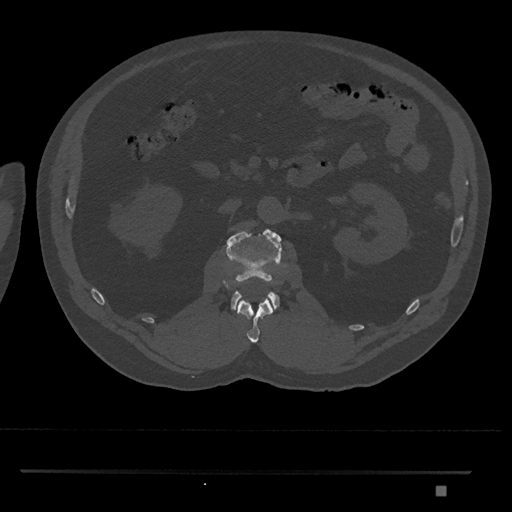
CT including the spine, one axial slice. Slice 788 of 1134 in the series (ordered by position). Reconstruction kernel Br40s/3. 120 kVp. Bone window (W 1800 / L 400 HU). 0.5 mm slice thickness. 512 × 512 image matrix, field of view 429 × 429 mm. Patient: male, 65 years. Case-level facts recorded for this patient, not image findings: primary cancer: prostate.
Outlined on this slice (semi-automatically segmented with operator editing):
- L1 vertebra: box from (x=237, y=297) to (x=274, y=343) px
- L2 vertebra: (x=226, y=229)–(x=282, y=311)